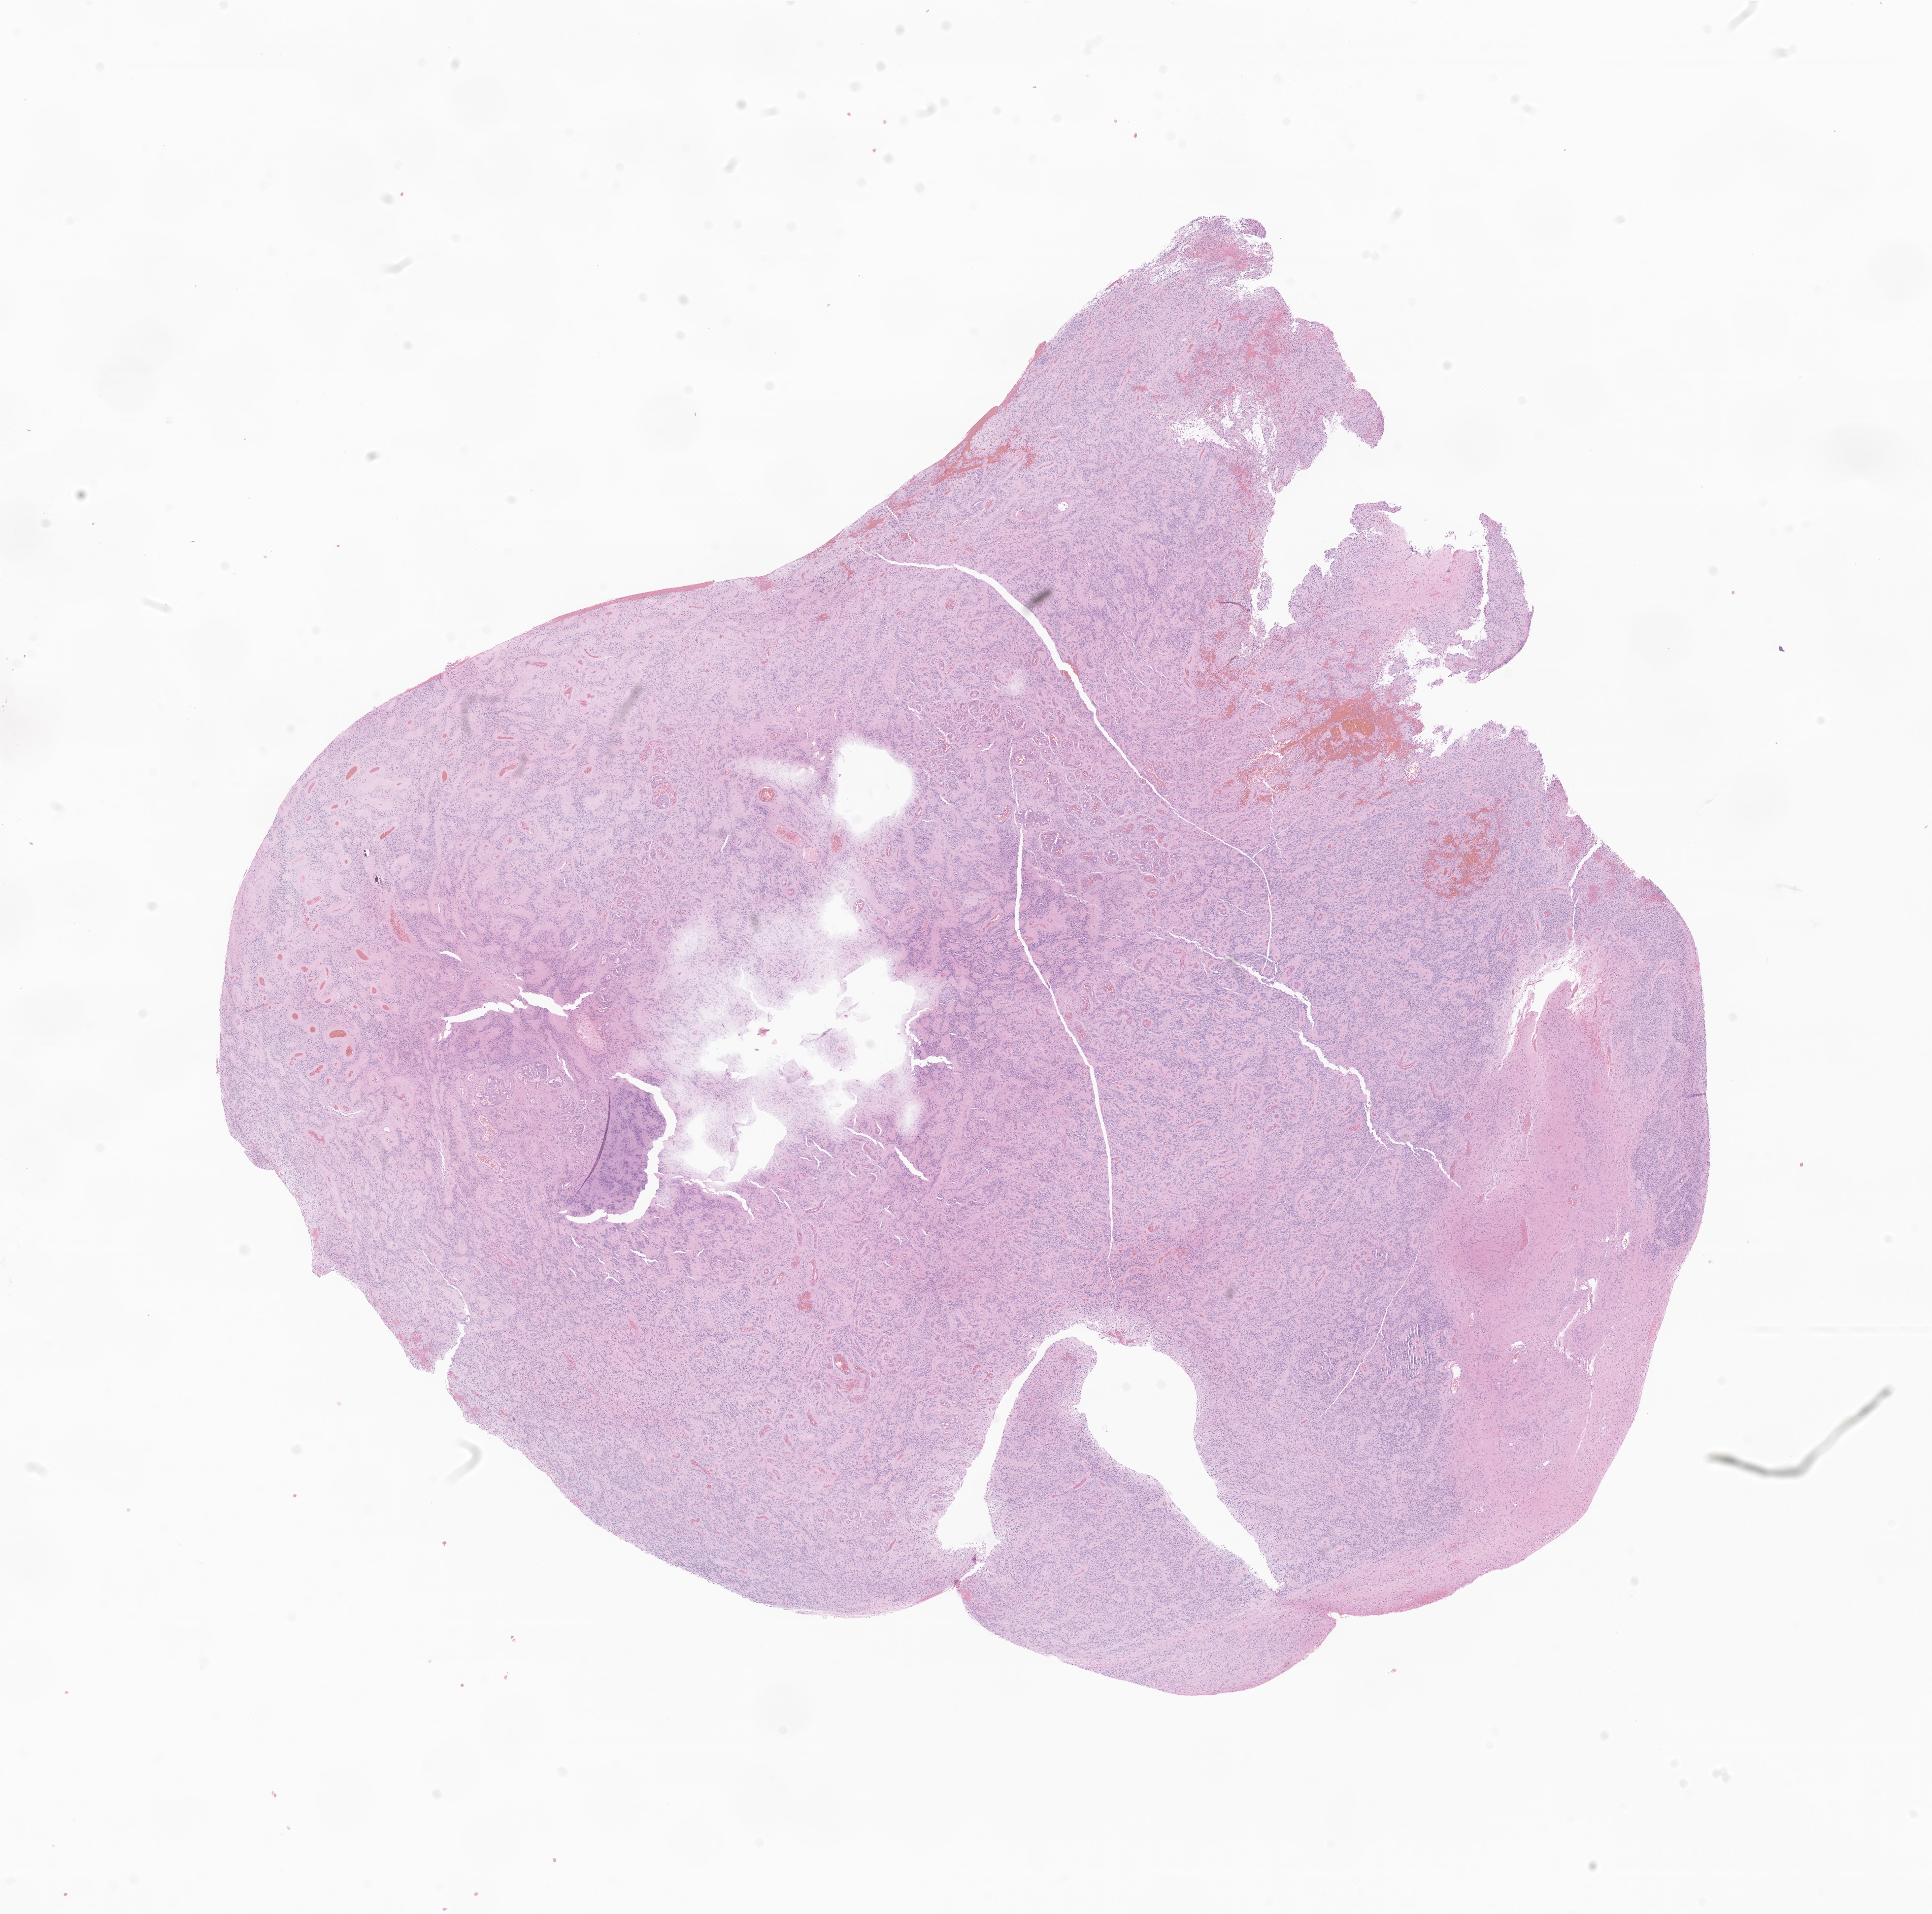
Hematoxylin and eosin (H&E) whole-slide image of tumor tissue from the brain — a low-resolution overview of the entire scanned area, about 16.5 x 16.4 mm; FFPE section. Patient female; age 868 days (about 2.4 years).
- diagnosis (ICD-O-3 morphology term): Ependymoma, NOS